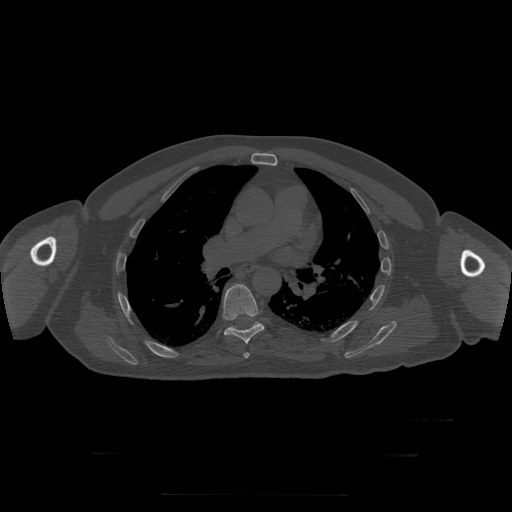
CT including the spine, one axial slice. Slice 186 of 397 in the series (ordered by position). Reconstruction kernel STANDARD. Bone window (W 1800 / L 400 HU). 1.25 mm slice thickness. 512 × 512 image matrix, field of view 510 × 510 mm. Patient age 73 years. Case-level facts recorded for this patient, not image findings: primary cancer: prostate.
Annotated regions visible in this slice (semi-automatic segmentation, software-assisted and operator-edited):
- T6 vertebra: bounding box (x1, y1, x2, y2) in pixels: (244, 353, 250, 359)
- T7 vertebra: (223, 284, 265, 345)
- T8 vertebra: (230, 322, 258, 330)